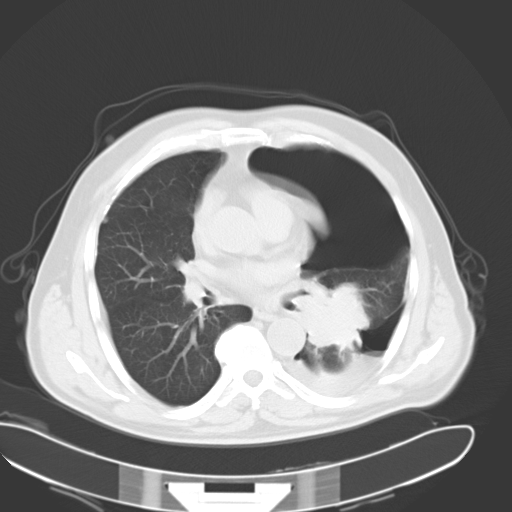
Chest CT, one axial slice; slice 19 of 34 in the series (ordered by position); reconstruction kernel B40f; 120 kVp; lung window (W 1500 / L -600 HU); 512 × 512 image matrix. Male patient, age 62 years. From the clinical record (not read from this slice): clinical TNM (as recorded): T3 N0 M1.
Annotated regions visible in this slice (rectangle marked by the reading radiologist):
- lung tumour (recorded histology: adenocarcinoma): bounding box [x1, y1, x2, y2] px = [292, 285, 372, 355]
- lung tumour (recorded histology: adenocarcinoma): [301, 278, 372, 352]